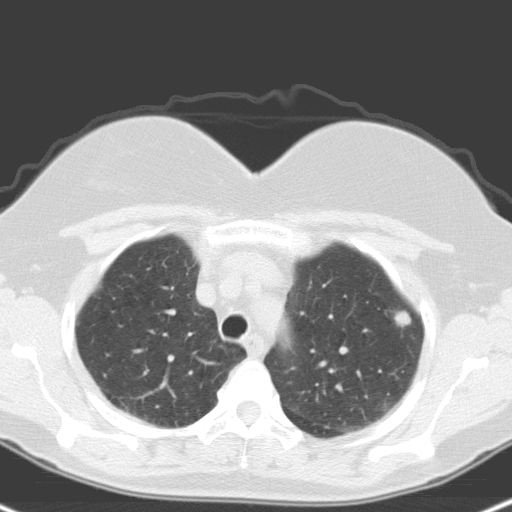
Low-dose screening chest CT, one axial slice. Slice 124 of 148 in the series (ordered by position). 120 kVp. Lung window (W 1500 / L -600 HU). 3.2 mm slice thickness. 512 × 512 image matrix, field of view 314 × 314 mm.
Structures marked on this image (manually delineated by an expert):
- lesion 1 (tumor, upper lobe of left lung): bounding box (x1, y1, x2, y2) in pixels: (394, 310, 411, 328)